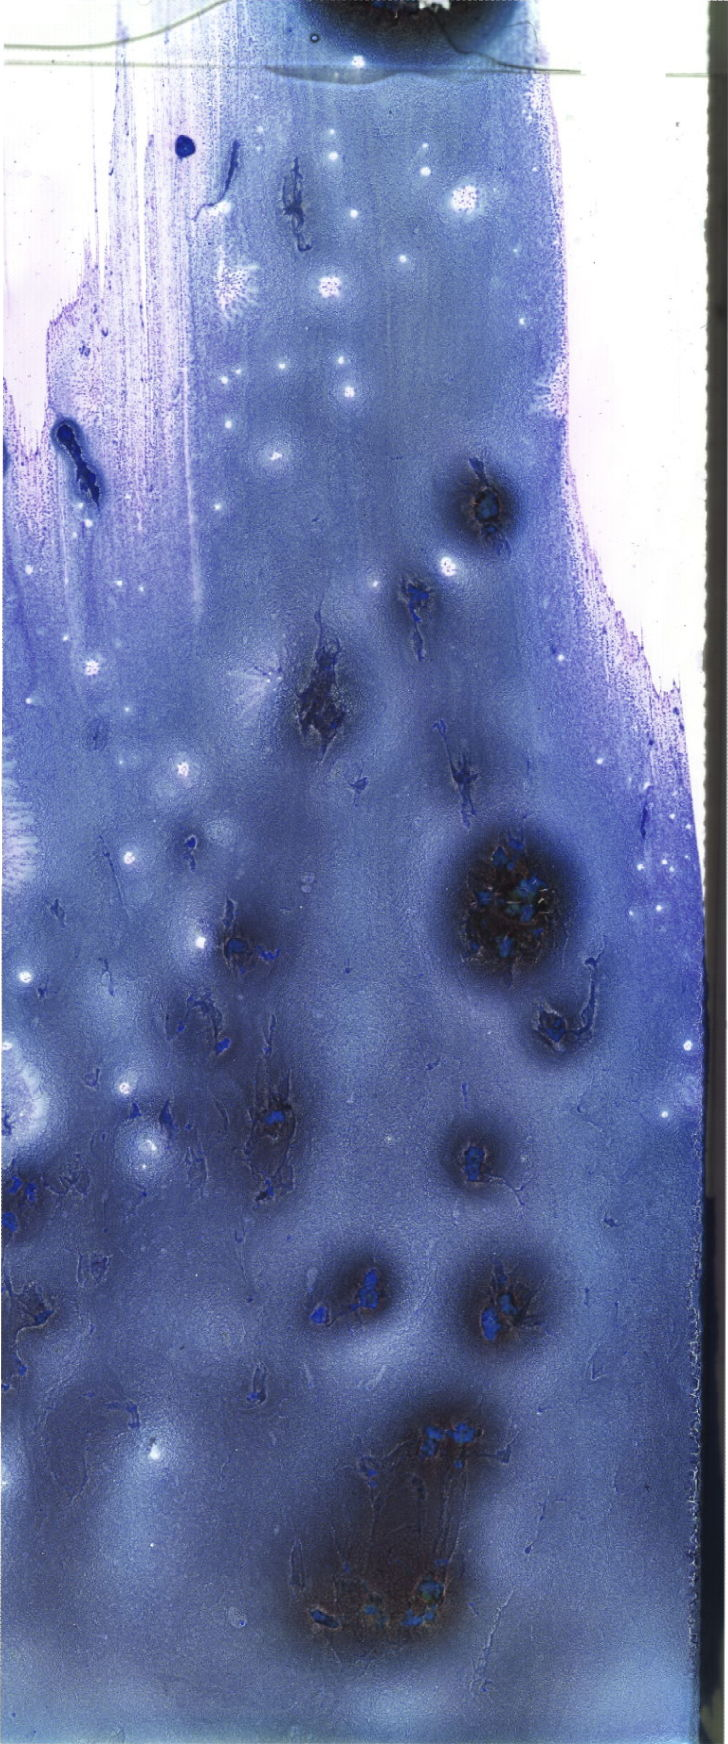
May-Grünwald-Giemsa (MGG)-stained marrow aspirate smear (whole slide) — low-resolution overview of the scanned area, about 20.6 x 49.4 mm. Patient sex: male.
Diagnosis: Acute Myeloid Leukemia with Maturation.